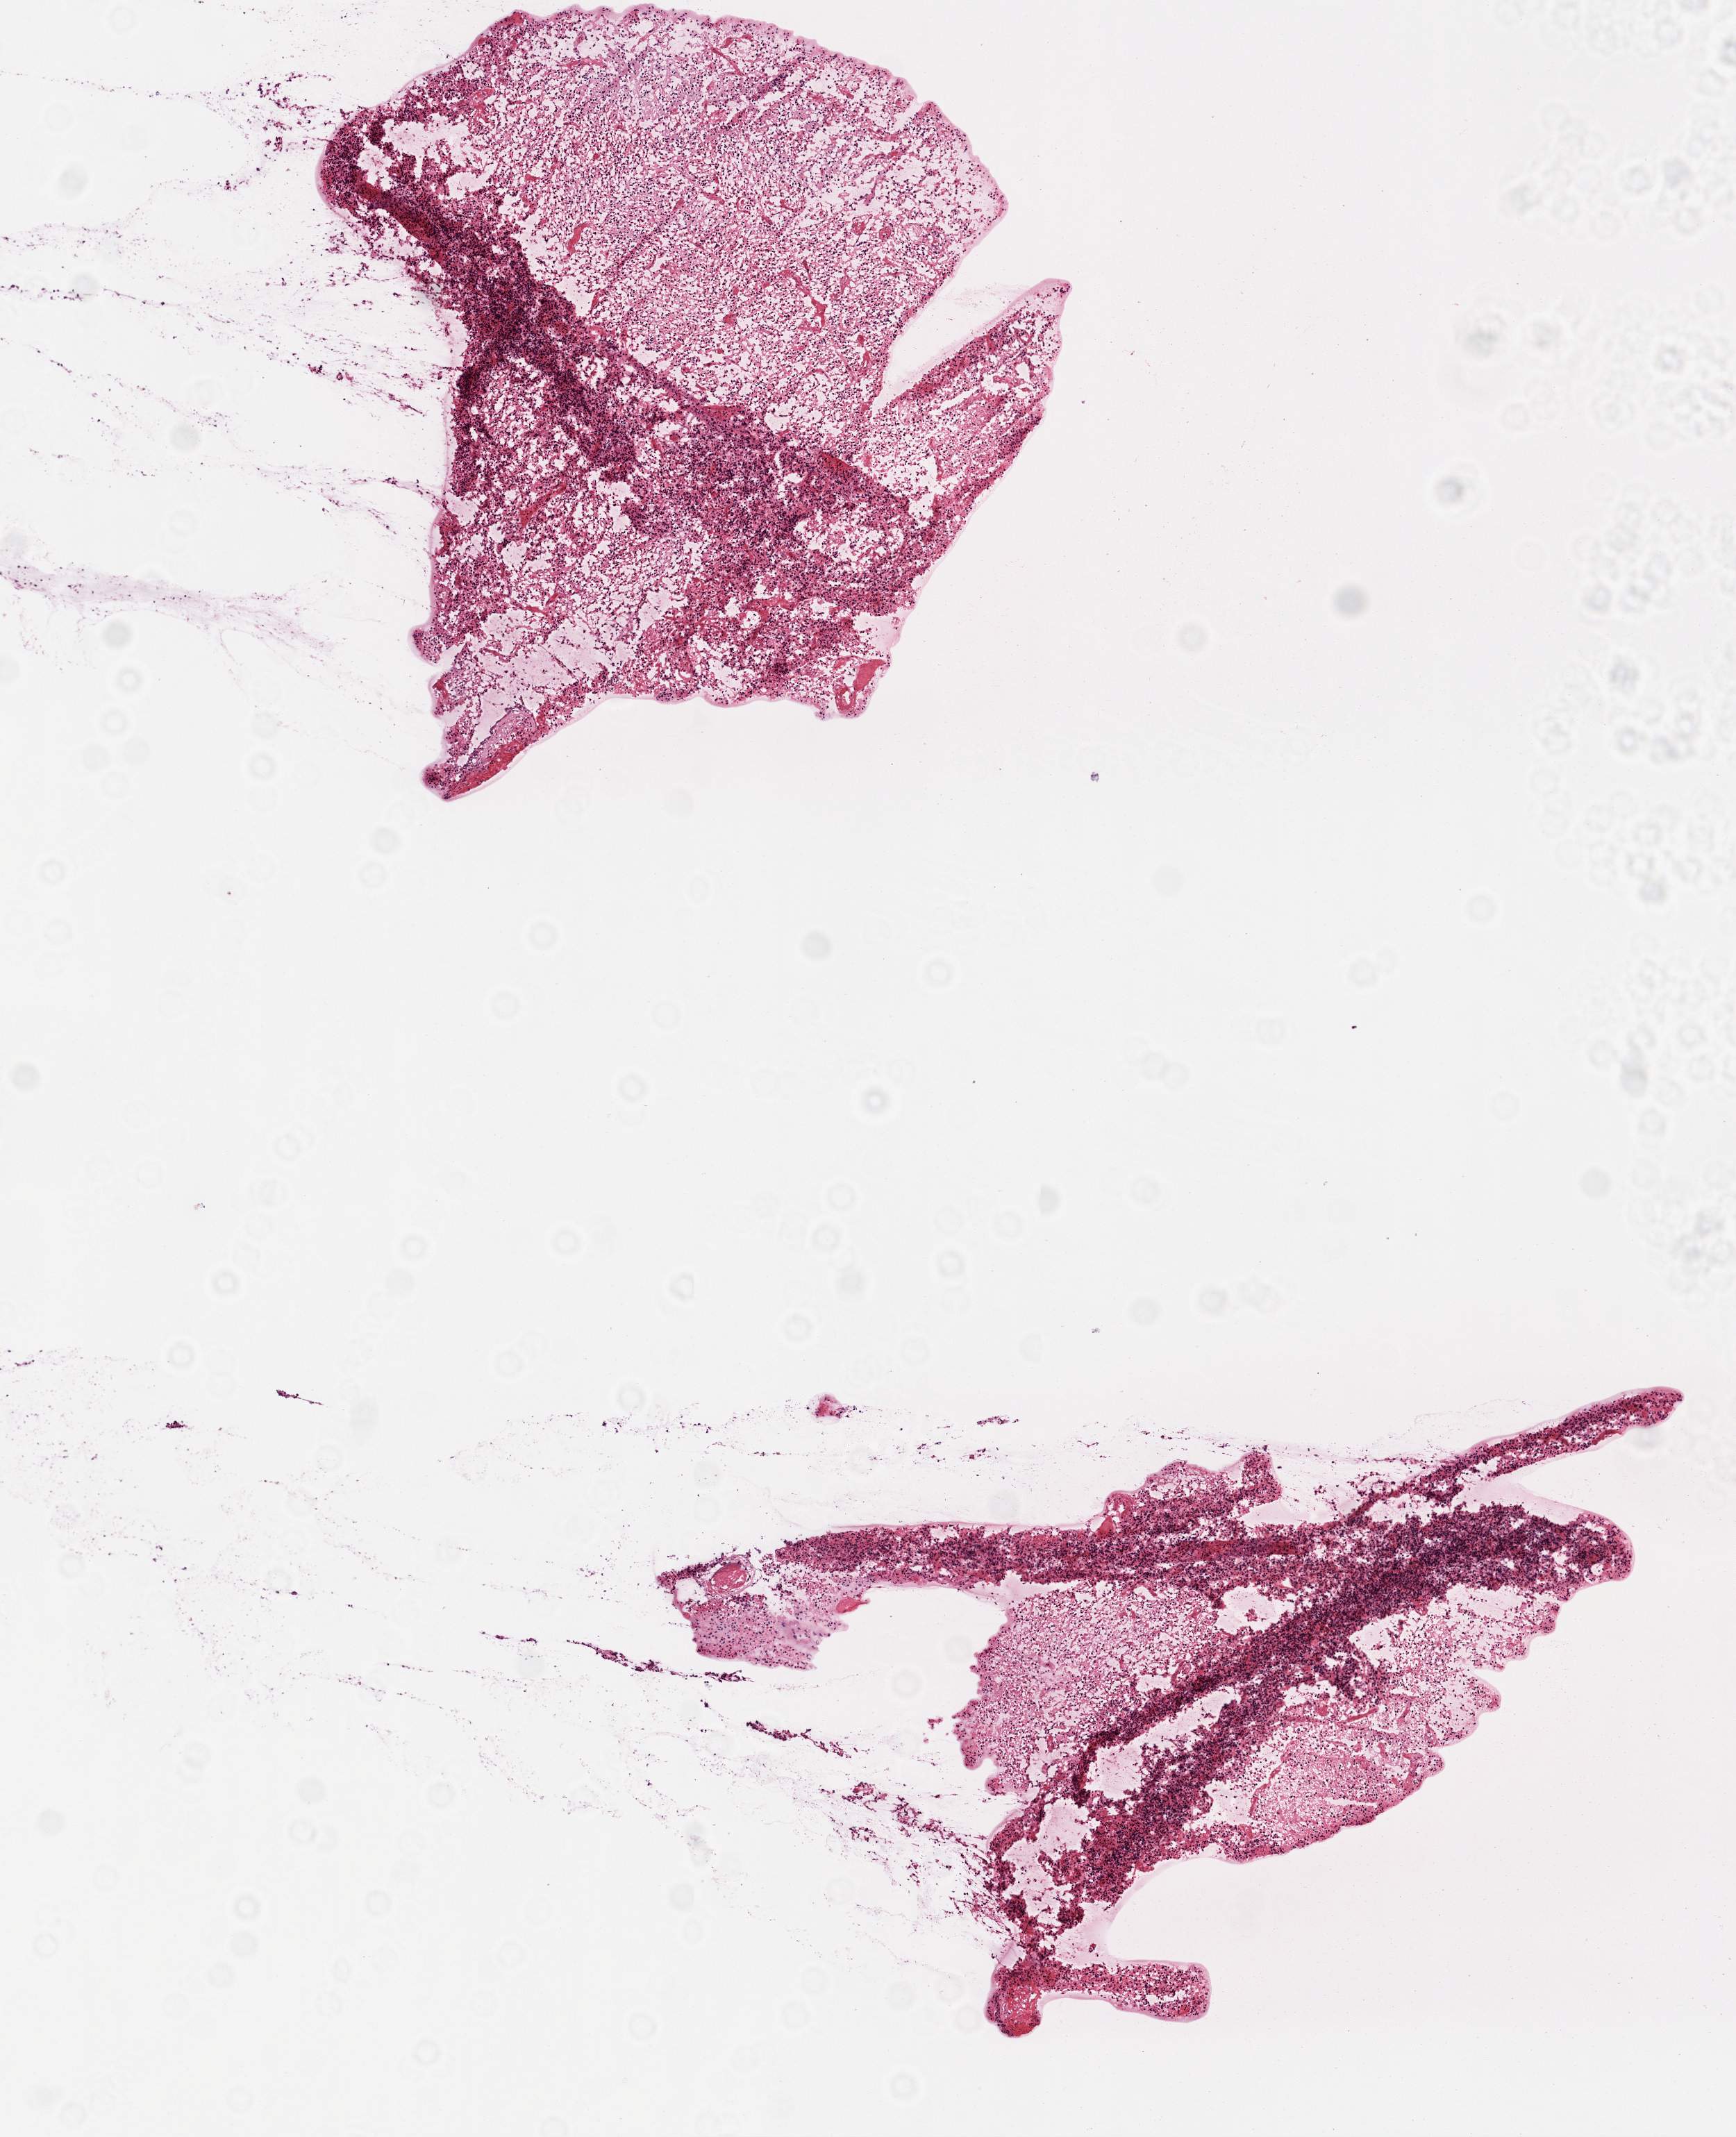
Whole-slide histology image, H&E-stained, low-resolution overview of the scanned area, about 5.0 x 6.2 mm (from a 20x scan). Frozen section. Sample: primary tumour, brain. Female, age 60 years at initial diagnosis. Slide review estimates, as recorded: tumour cells 80%, tumour nuclei 85%, normal cells 10%, stromal cells 10%, necrosis 0%.
Histologic diagnosis: Glioblastoma.